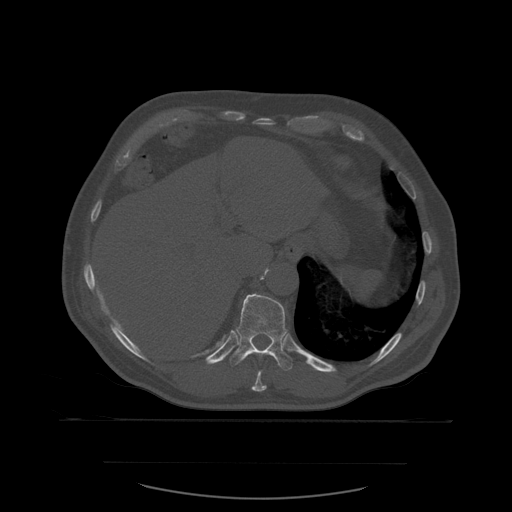
CT including the spine, one axial slice. Slice 302 of 590 in the series (ordered by position). Bone window (W 1800 / L 400 HU). 1.25 mm slice thickness. 512 × 512 image matrix. Patient age 71 years. From the clinical record (not read from this slice): primary cancer: lung.
Outlined on this slice (semi-automatic segmentation, software-assisted and operator-edited):
- T10 vertebra: bounding box <252,371,267,392> (left, top, right, bottom; pixels)
- T11 vertebra: <230,294,294,371>